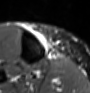
MRI of an extremity soft-tissue mass, one axial slice; position 17 of 60 along the scan axis; STIR; MR volume resampled by the dataset authors to the PET/CT grid (not the native acquisition matrix); 3.27 mm slice thickness; 90 × 93 image matrix, field of view 88 × 91 mm. Female patient. From the clinical record (not read from this slice): histological type: undifferentiated – high grade; grade: high; site of the primary tumour: right thigh.
Annotated regions visible in this slice (expert contour drawn on MRI and transferred to this co-registered scan by the dataset authors):
- gross tumour volume (mass): bounding box [x1, y1, x2, y2] px = [35, 30, 57, 54]